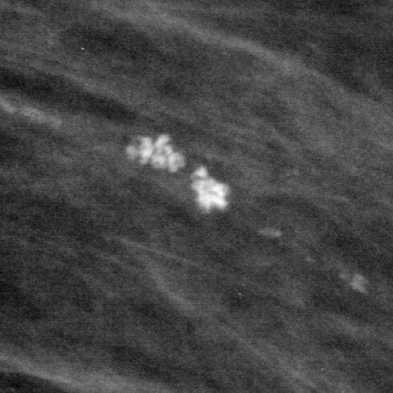
Region of interest cut from a scanned film mammogram (one marked finding), left breast, MLO view, BI-RADS breast density category 2 (scale 1–4).
- Marked abnormality: calcifications, morphology pleomorphic, distribution clustered; BI-RADS assessment category 4; subtlety rating 5 on a 1 (subtle) to 5 (obvious) scale; pathology result (as recorded, not read from the image): benign.